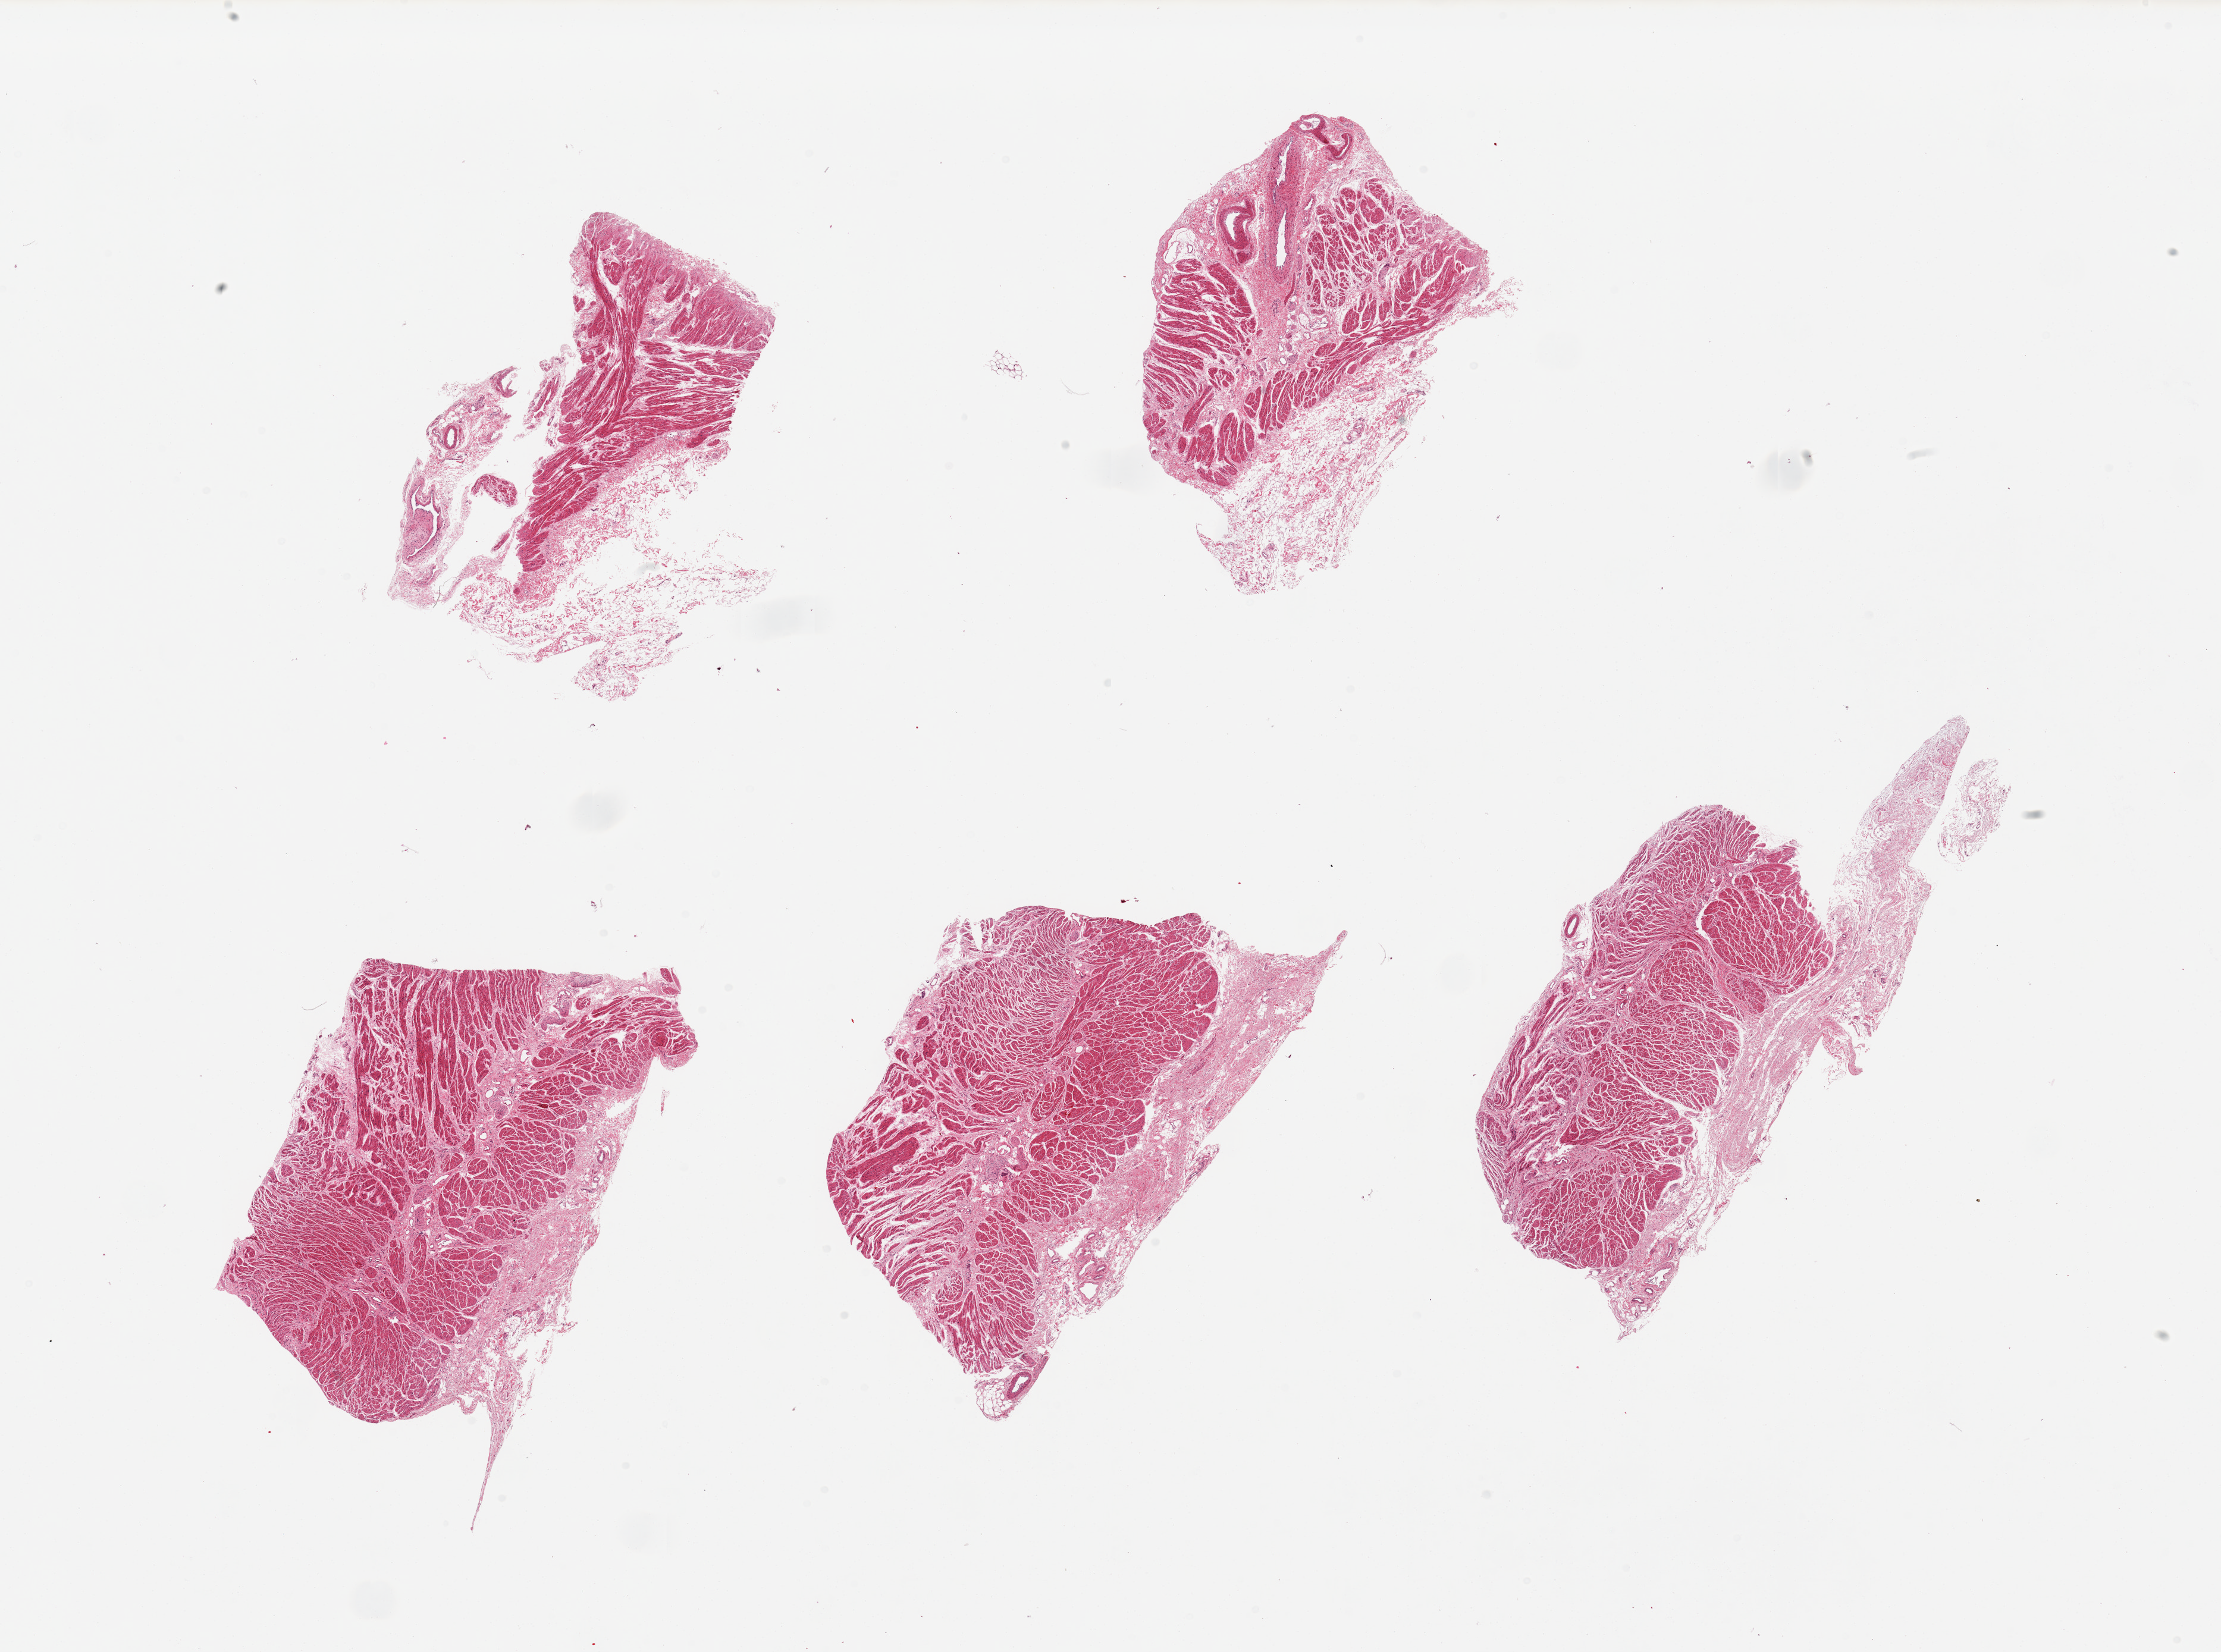
Whole-slide image, hematoxylin and eosin (H&E) stain, brightfield — low-resolution overview of the scanned area, about 29.5 x 22.0 mm, PAXgene-fixed paraffin-embedded (PFPE) section, section of gastroesophageal junction (target tissue), donor tissue sample. Donor: female.
* reviewer comment on this tissue sample: 6 pieces, all muscularis; good specimens; adherent serosa on all, 1-2mm